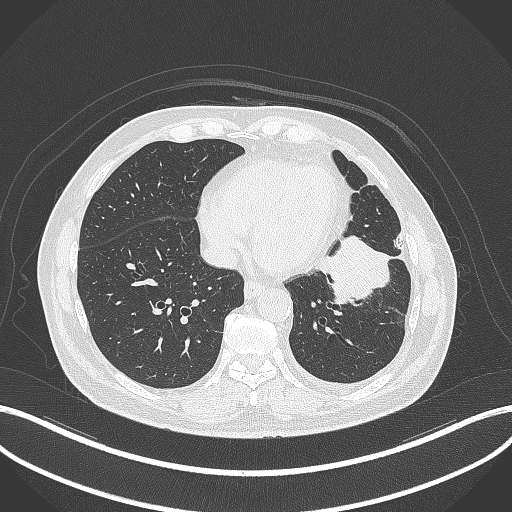
Chest CT, one axial slice; slice 117 of 230 in the series (ordered by position); 120 kVp; lung window (W 1500 / L -600 HU); 1 mm slice thickness; 512 × 512 image matrix, field of view 400 × 400 mm. Patient: male, 68 years. From the clinical record (not read from this slice): clinical TNM (as recorded): T2b N0 M0.
Structures marked on this image (bounding box drawn by a radiologist):
- lung tumour (recorded histology: squamous cell carcinoma): bounding box [x1, y1, x2, y2] px = [317, 229, 394, 313]